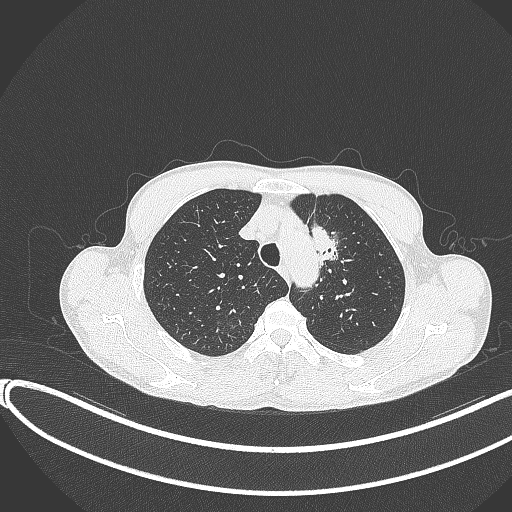
Chest CT, one axial slice. Slice 303 of 374 in the series (ordered by position). 120 kVp. Lung window (W 1500 / L -600 HU). 1 mm slice thickness. 512 × 512 image matrix, field of view 400 × 400 mm. Male patient, age 58 years. From the clinical record (not read from this slice): clinical TNM (as recorded): T1c N1 M0.
Structures marked on this image (rectangle marked by the reading radiologist):
- lung tumour (recorded histology: adenocarcinoma): bounding box [x1, y1, x2, y2] px = [305, 221, 347, 274]